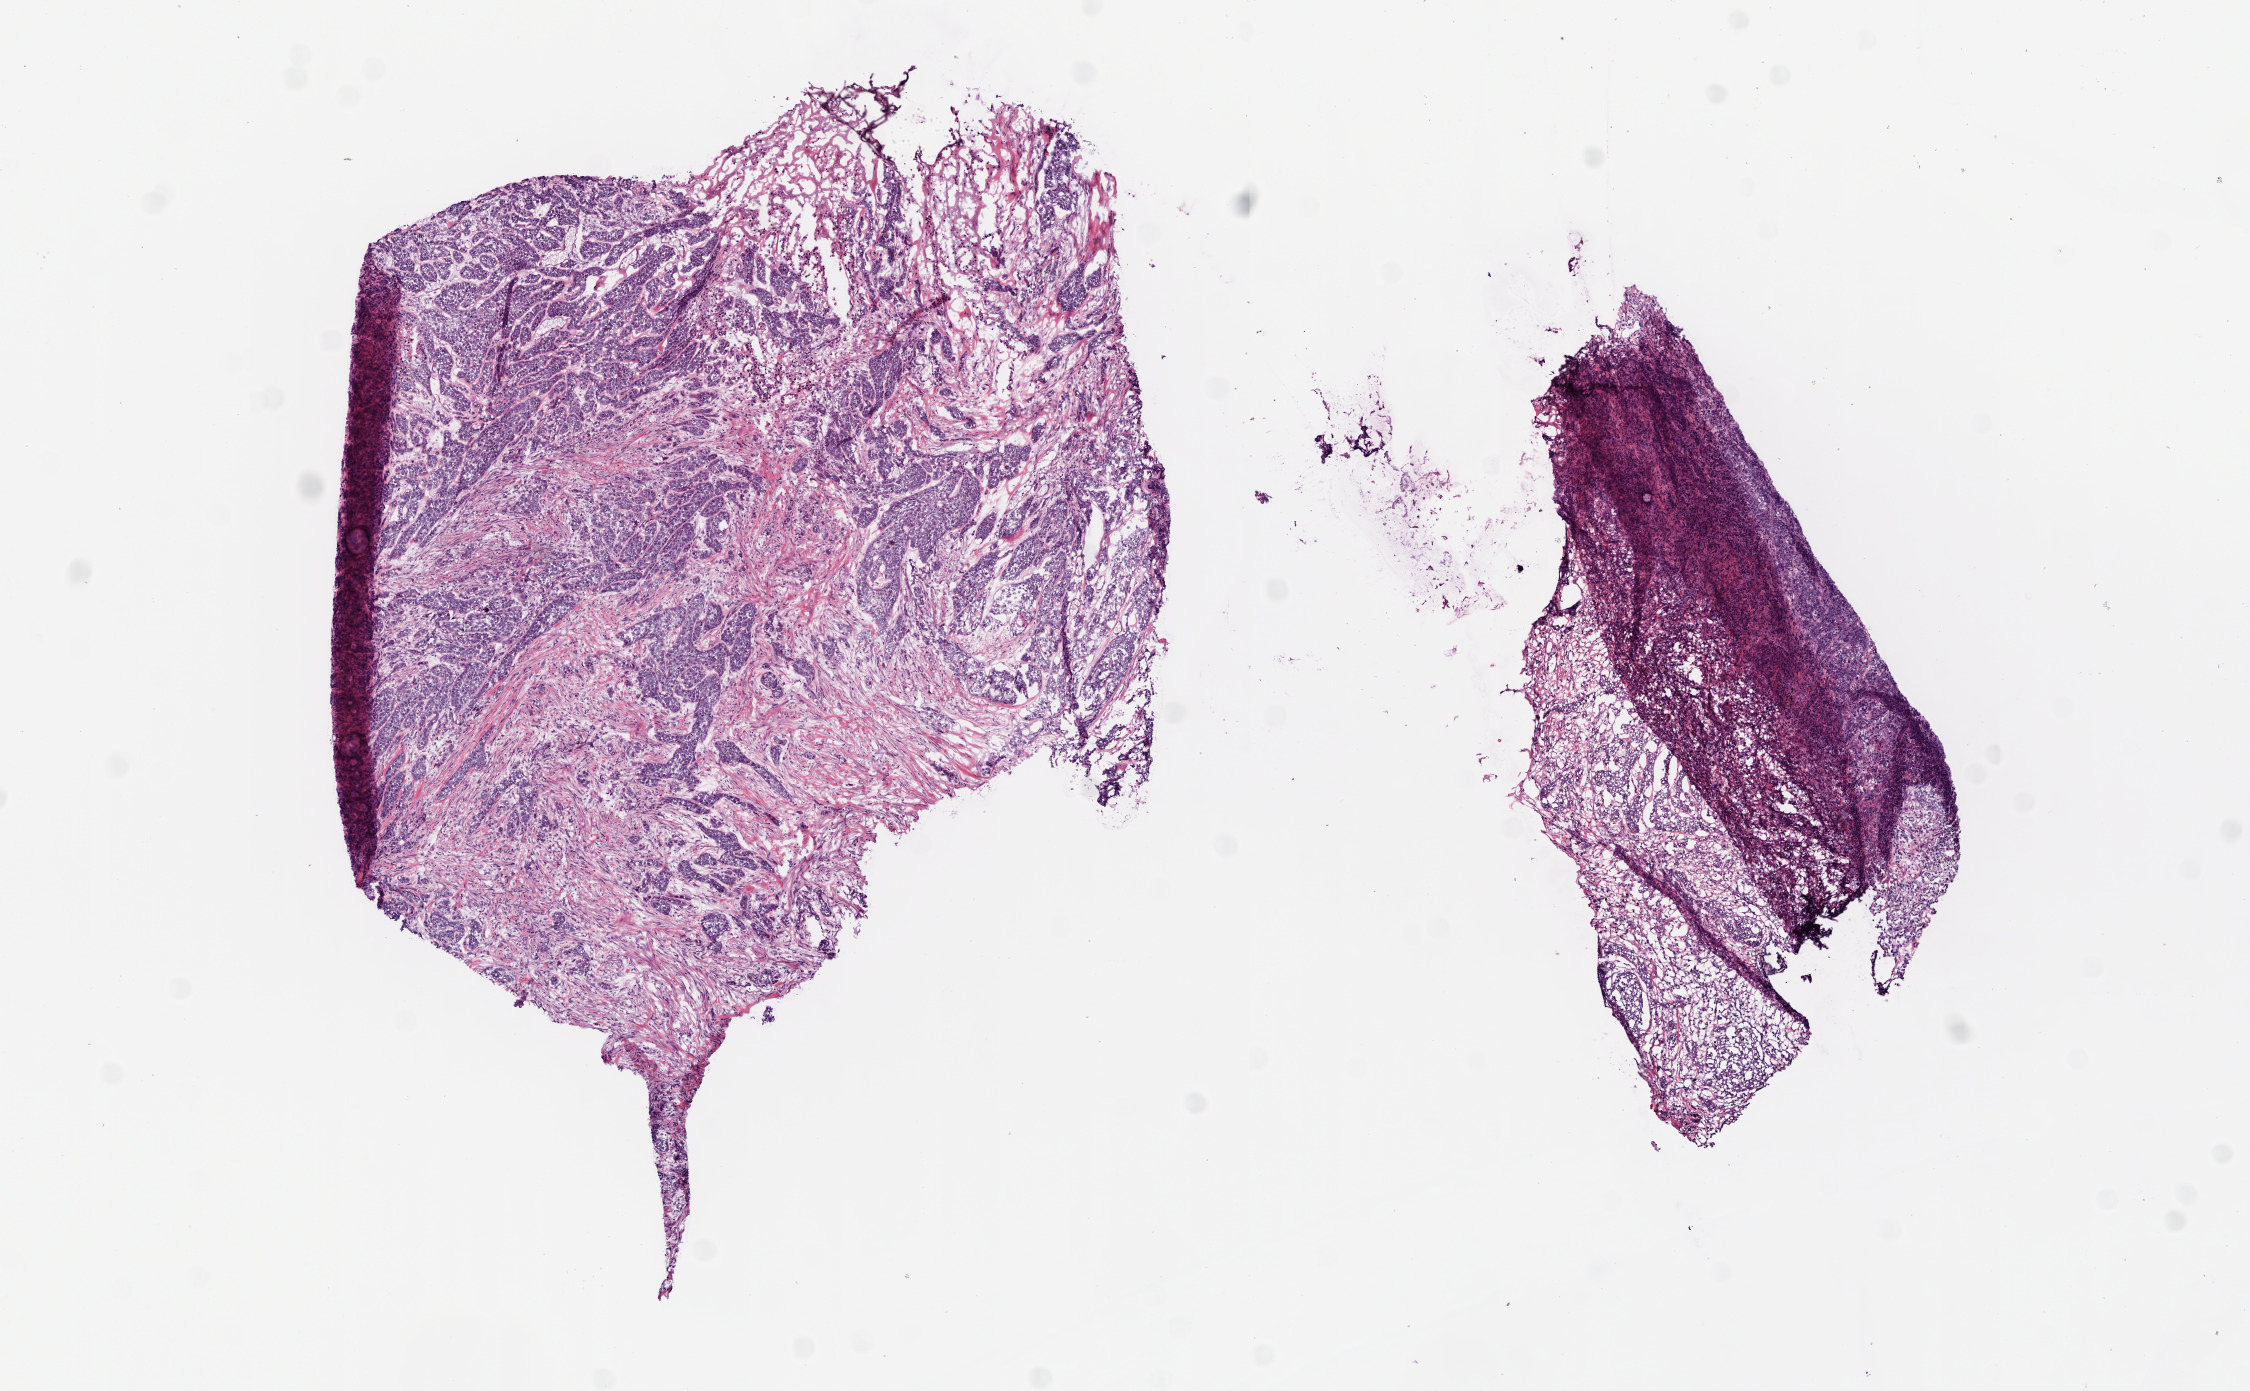
Whole-slide histology image, Hematoxylin and eosin (H&E) stained, low-resolution overview of the scanned area, about 9.0 x 5.6 mm (slide scanned at 20x); frozen section from the bottom of the tissue portion; sample: primary tumour, lung. Patient: male, age at initial diagnosis 75 years. Pathologist review of this section (percent, as recorded): tumour cells 70%, tumour nuclei 70%.
Histologic diagnosis: Squamous cell carcinoma, NOS.